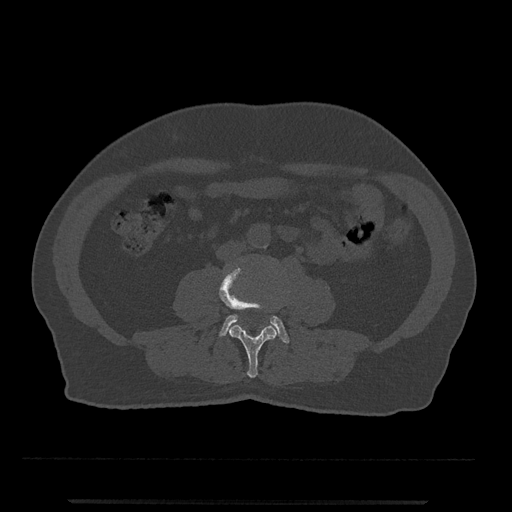
CT including the spine, one axial slice; slice 177 of 797 in the series (ordered by position); reconstruction kernel Br40s/3; 120 kVp; bone window (W 1800 / L 400 HU); 0.5 mm slice thickness; 512 × 512 image matrix, field of view 419 × 419 mm. Patient: male, 63 years. From the clinical record (not read from this slice): primary cancer: prostate.
Annotated regions visible in this slice (semi-automatic segmentation, software-assisted and operator-edited):
- L3 vertebra: bounding box (x1, y1, x2, y2) in pixels: (219, 266, 277, 378)
- L4 vertebra: (219, 315, 289, 343)